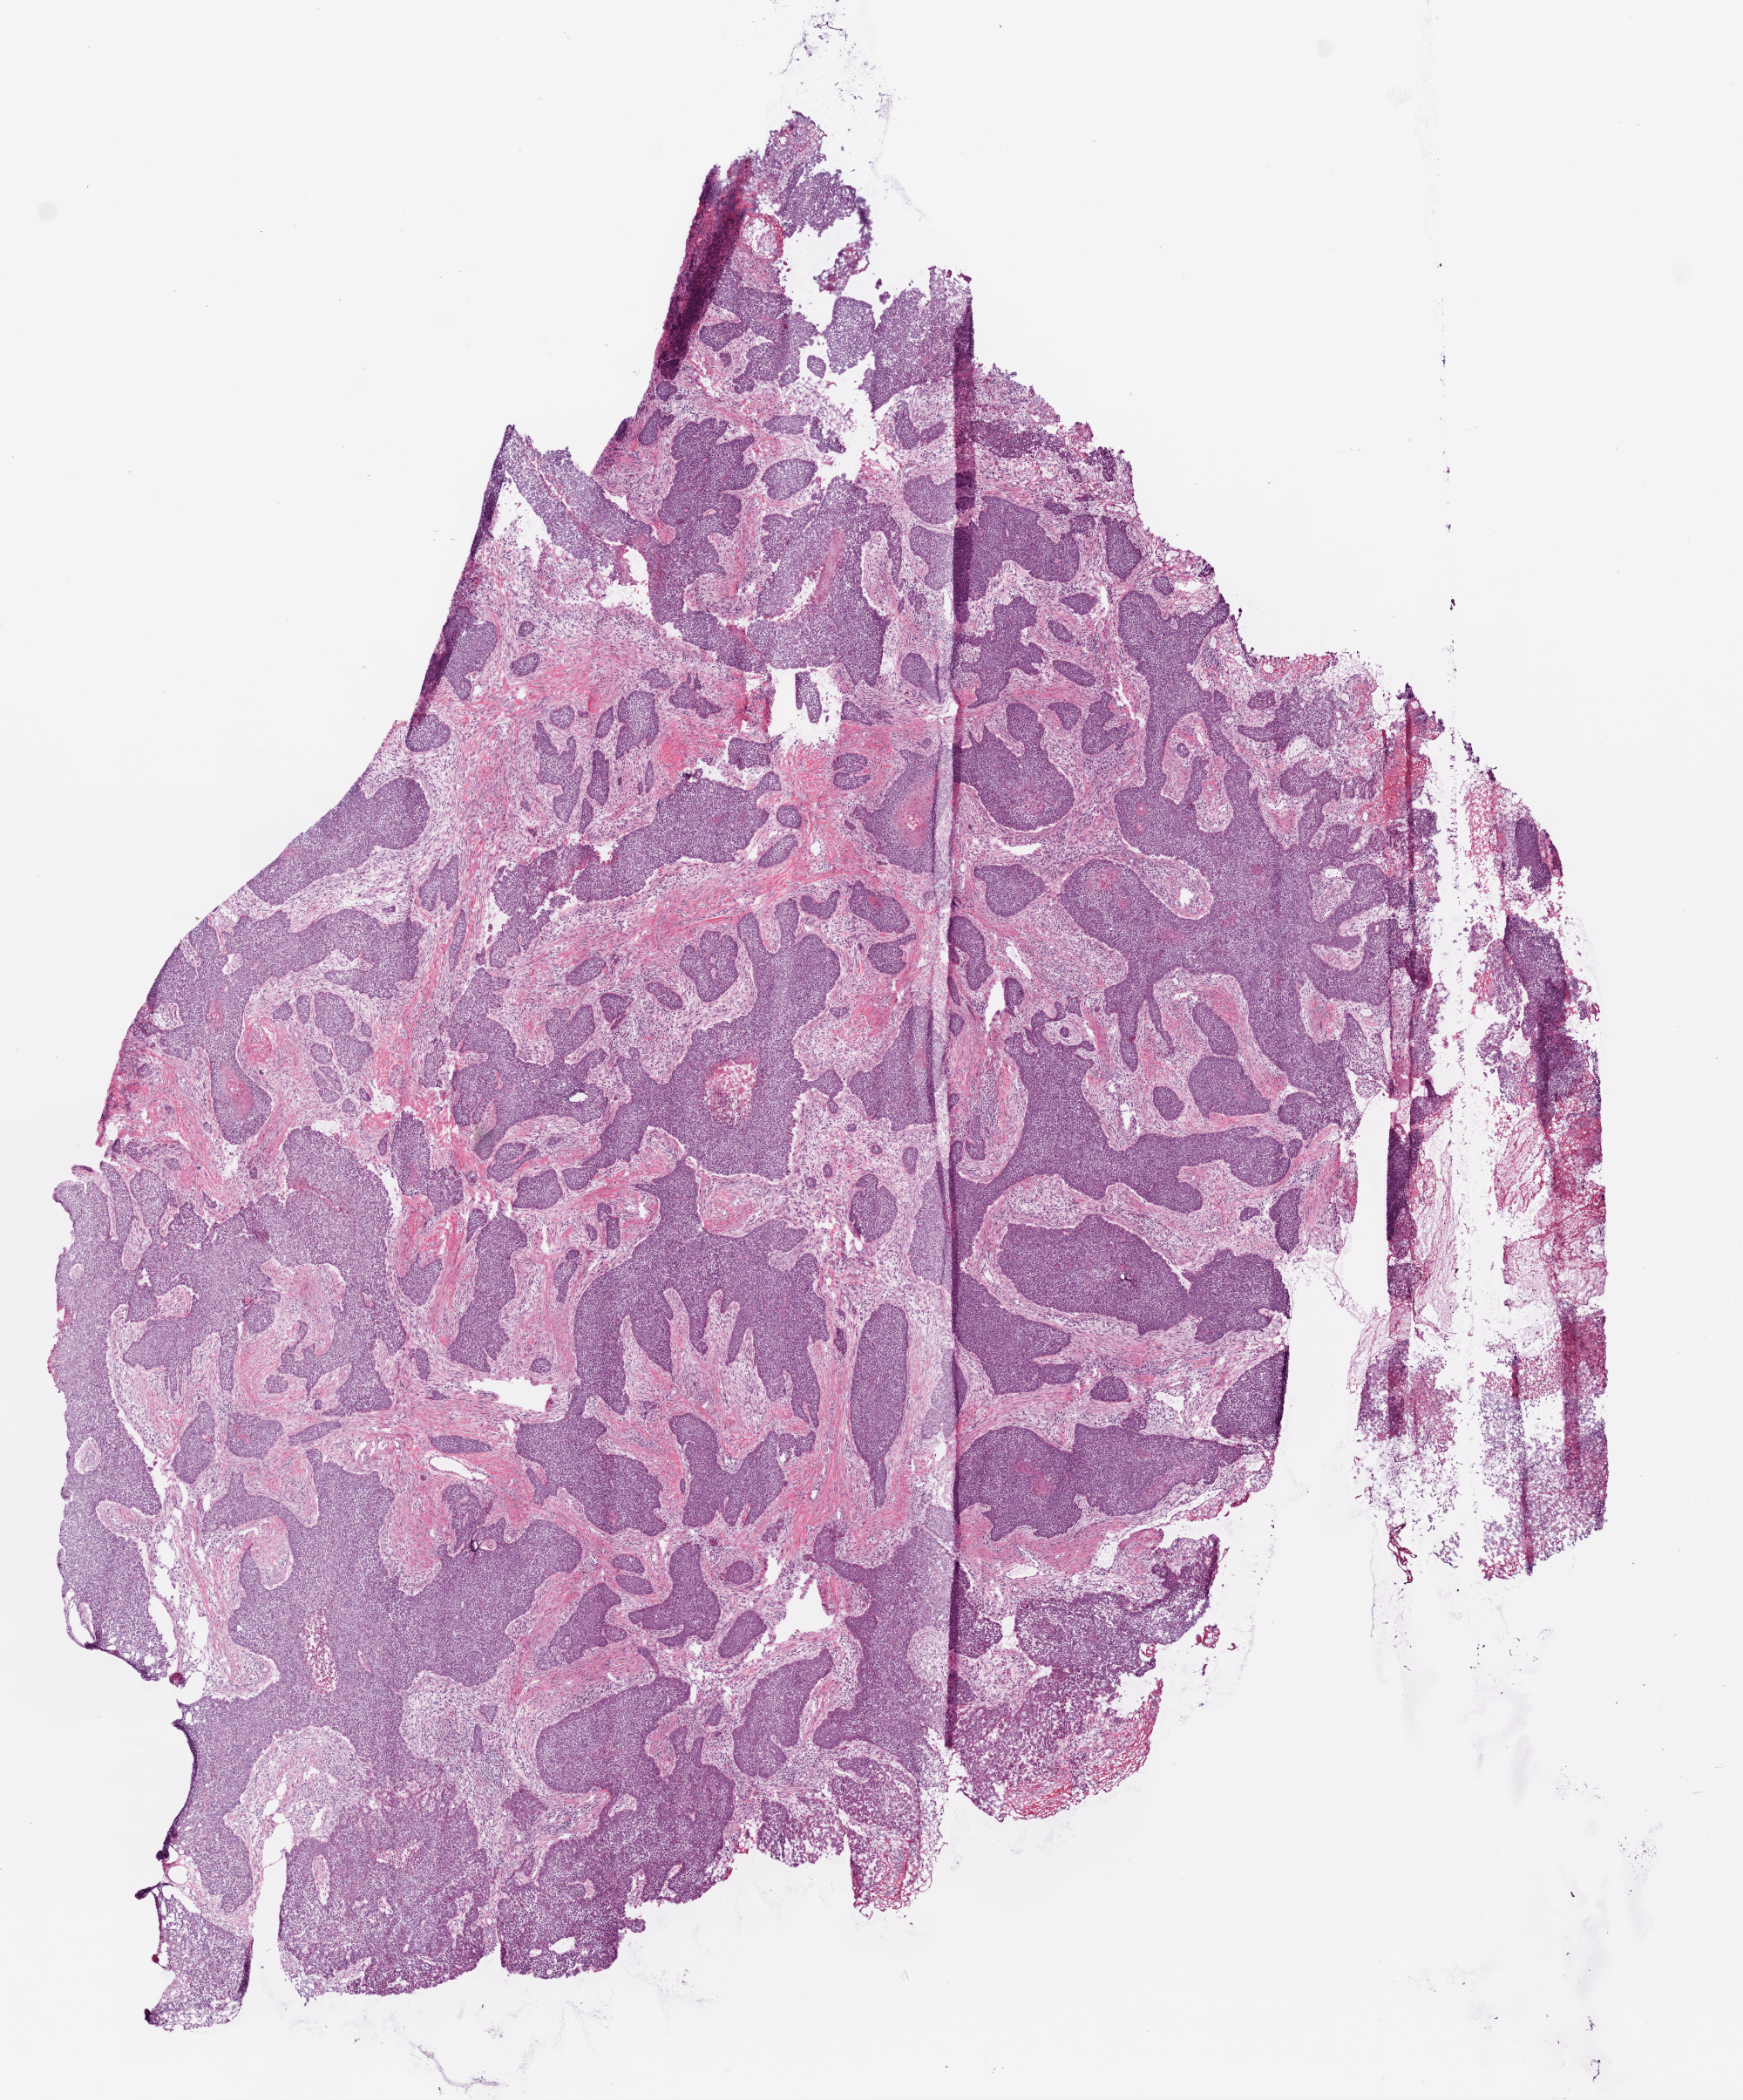
Whole-slide histology image, H&E-stained, low-resolution overview of the scanned area, about 8.0 x 9.7 mm (from a 20x scan); frozen section from the bottom of the tissue portion; primary tumour sample from the head and neck. Male, age 83 years at initial diagnosis.
Diagnosis: Squamous cell carcinoma, NOS (larynx, NOS).